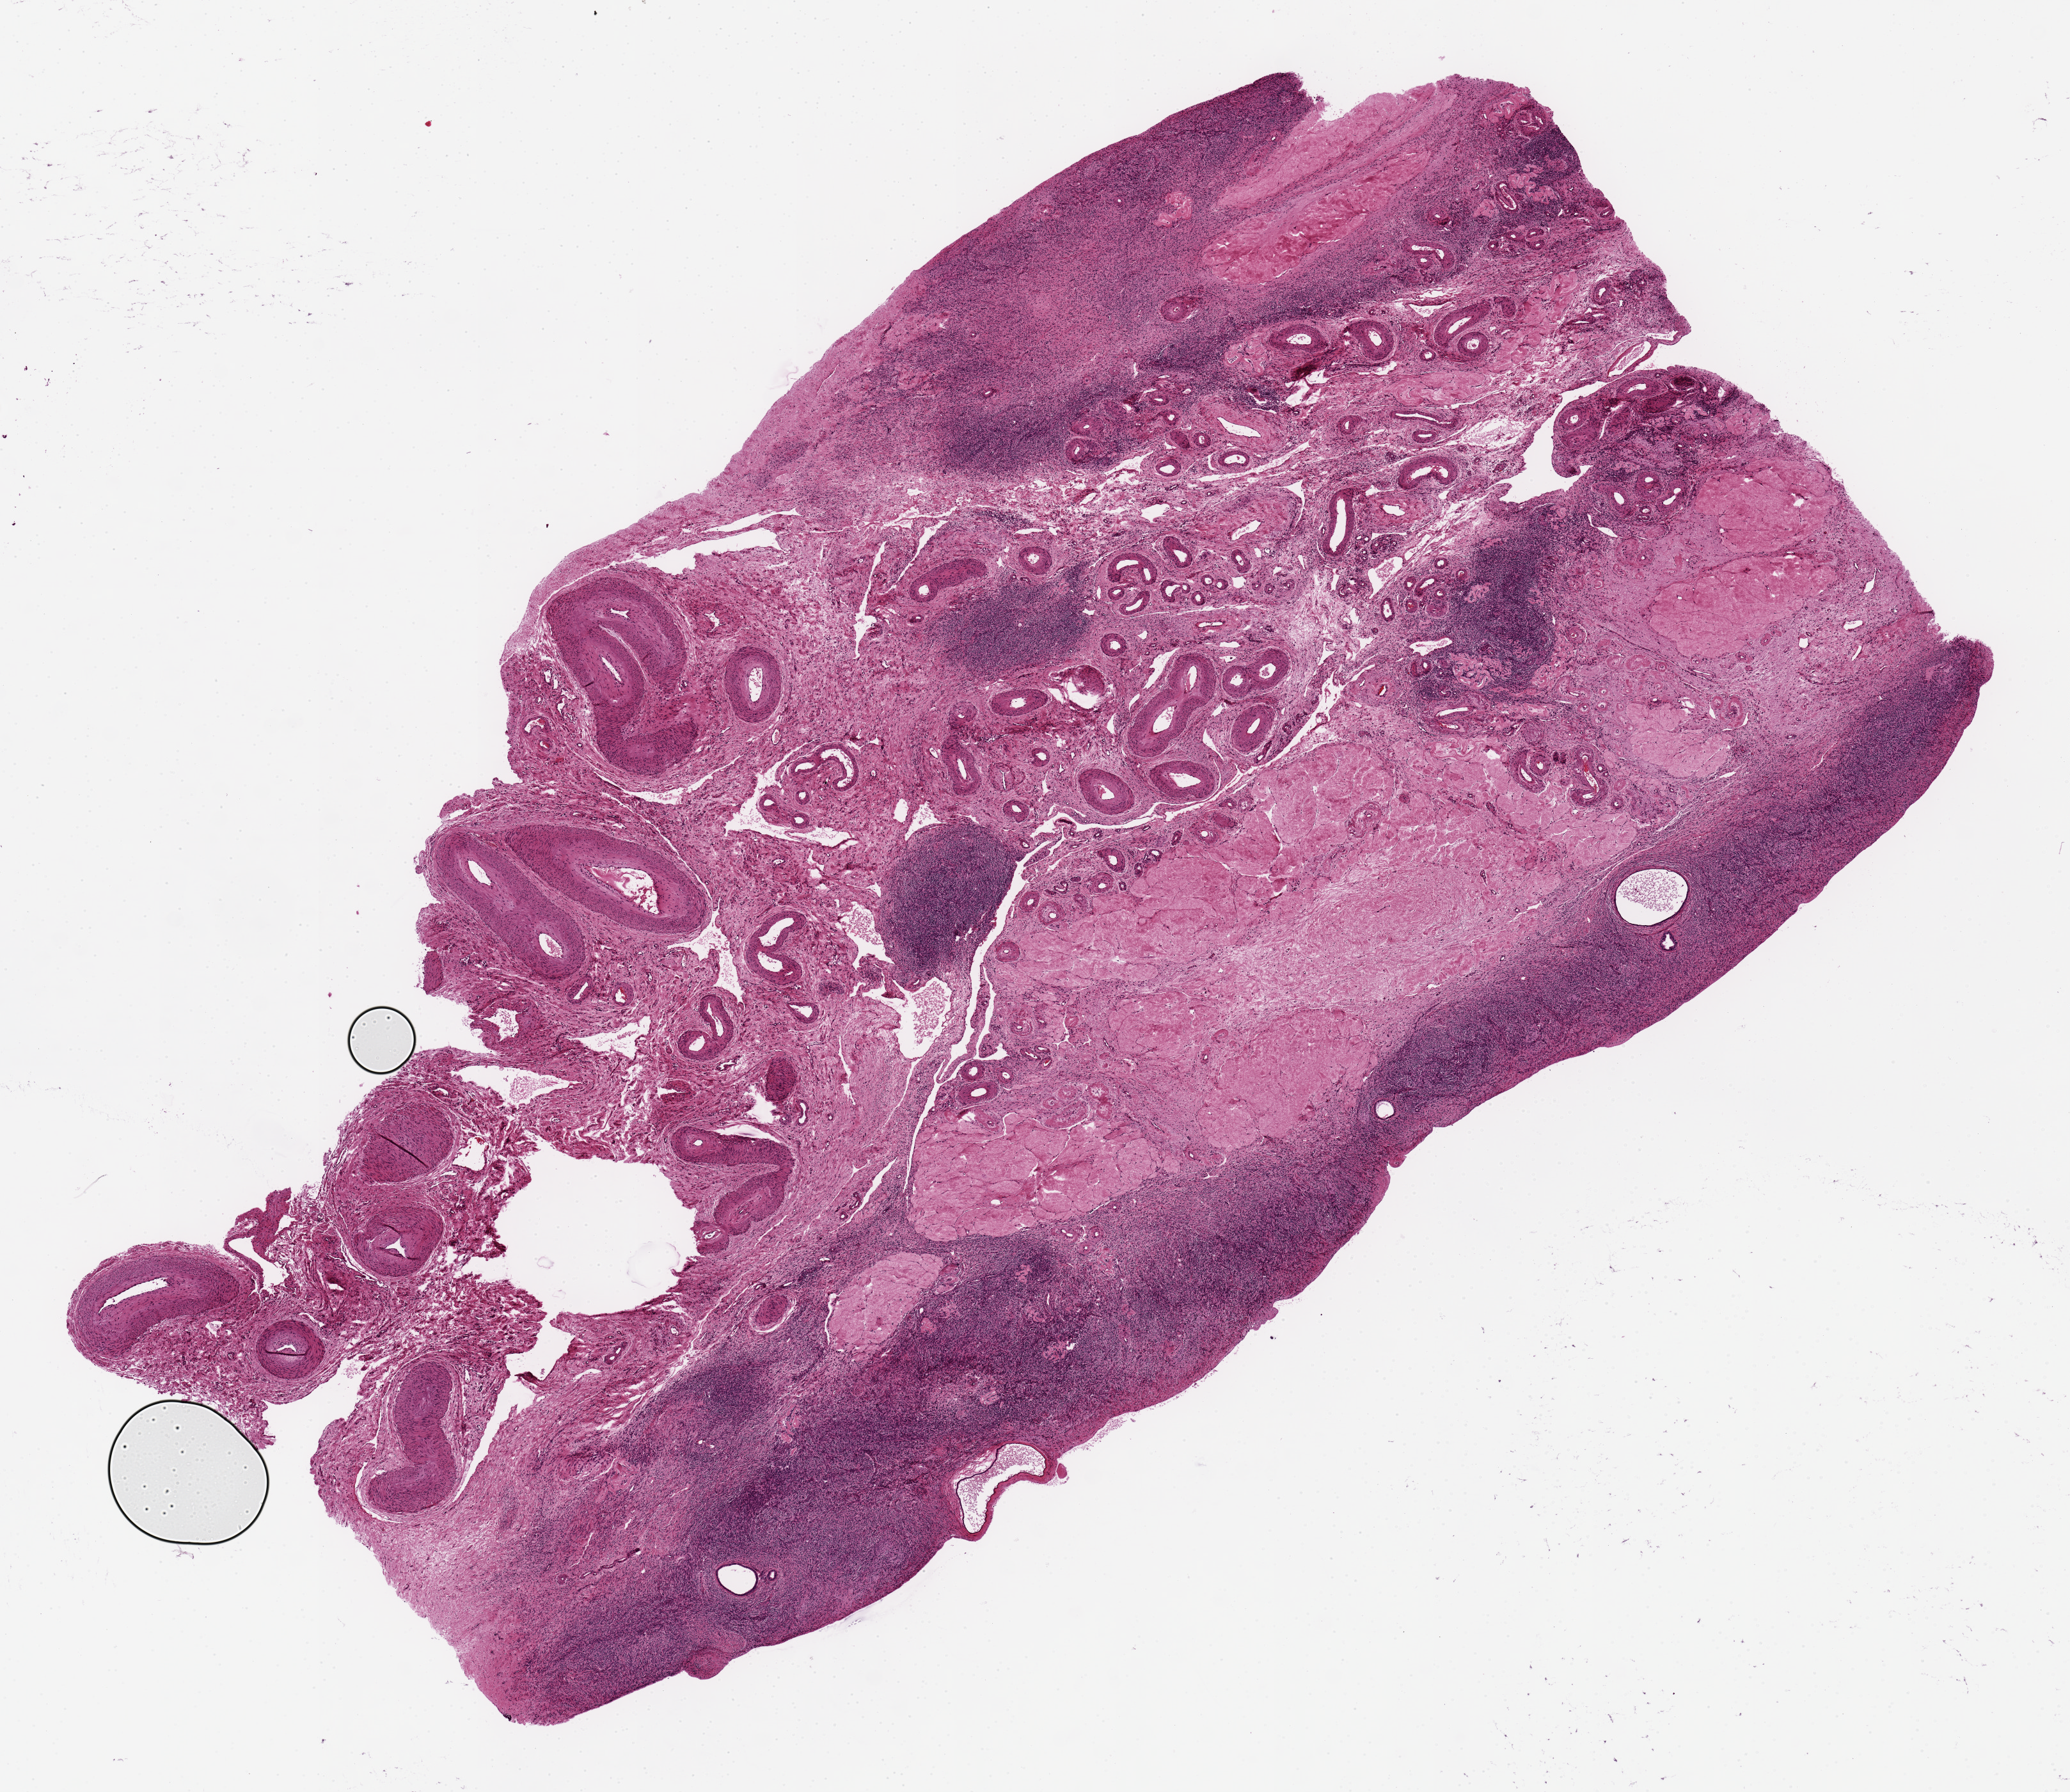
Whole-slide image, H&E stain — whole scanned area (about 12.8 x 11.1 mm) shown as a low-resolution overview, PAXgene-fixed, paraffin-embedded tissue, section of ovary (target tissue), donor tissue sample. Donor sex: female.
Review note (as recorded): parenchyma ~20%.